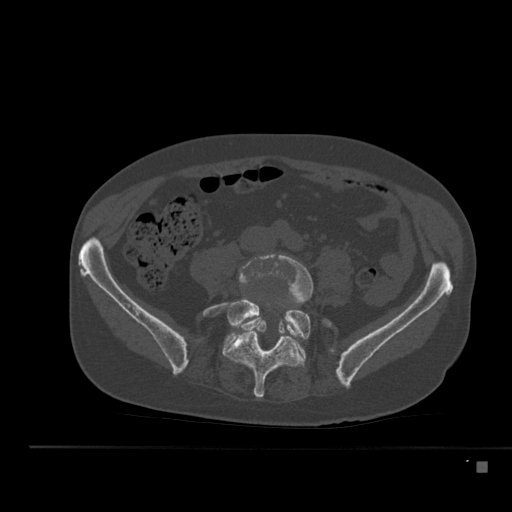
CT including the spine, one axial slice. Slice 130 of 517 in the series (ordered by position). Reconstruction kernel Br40s. 120 kVp. Bone window (W 1800 / L 400 HU). 1.5 mm slice thickness. 512 × 512 image matrix, field of view 408 × 408 mm. Patient: male, 70 years. From the clinical record (not read from this slice): primary cancer: renal.
Annotated regions visible in this slice (semi-automatically segmented with operator editing):
- L4 vertebra: bounding box (x1, y1, x2, y2) in pixels: (238, 254, 313, 340)
- L5 vertebra: (203, 299, 330, 398)